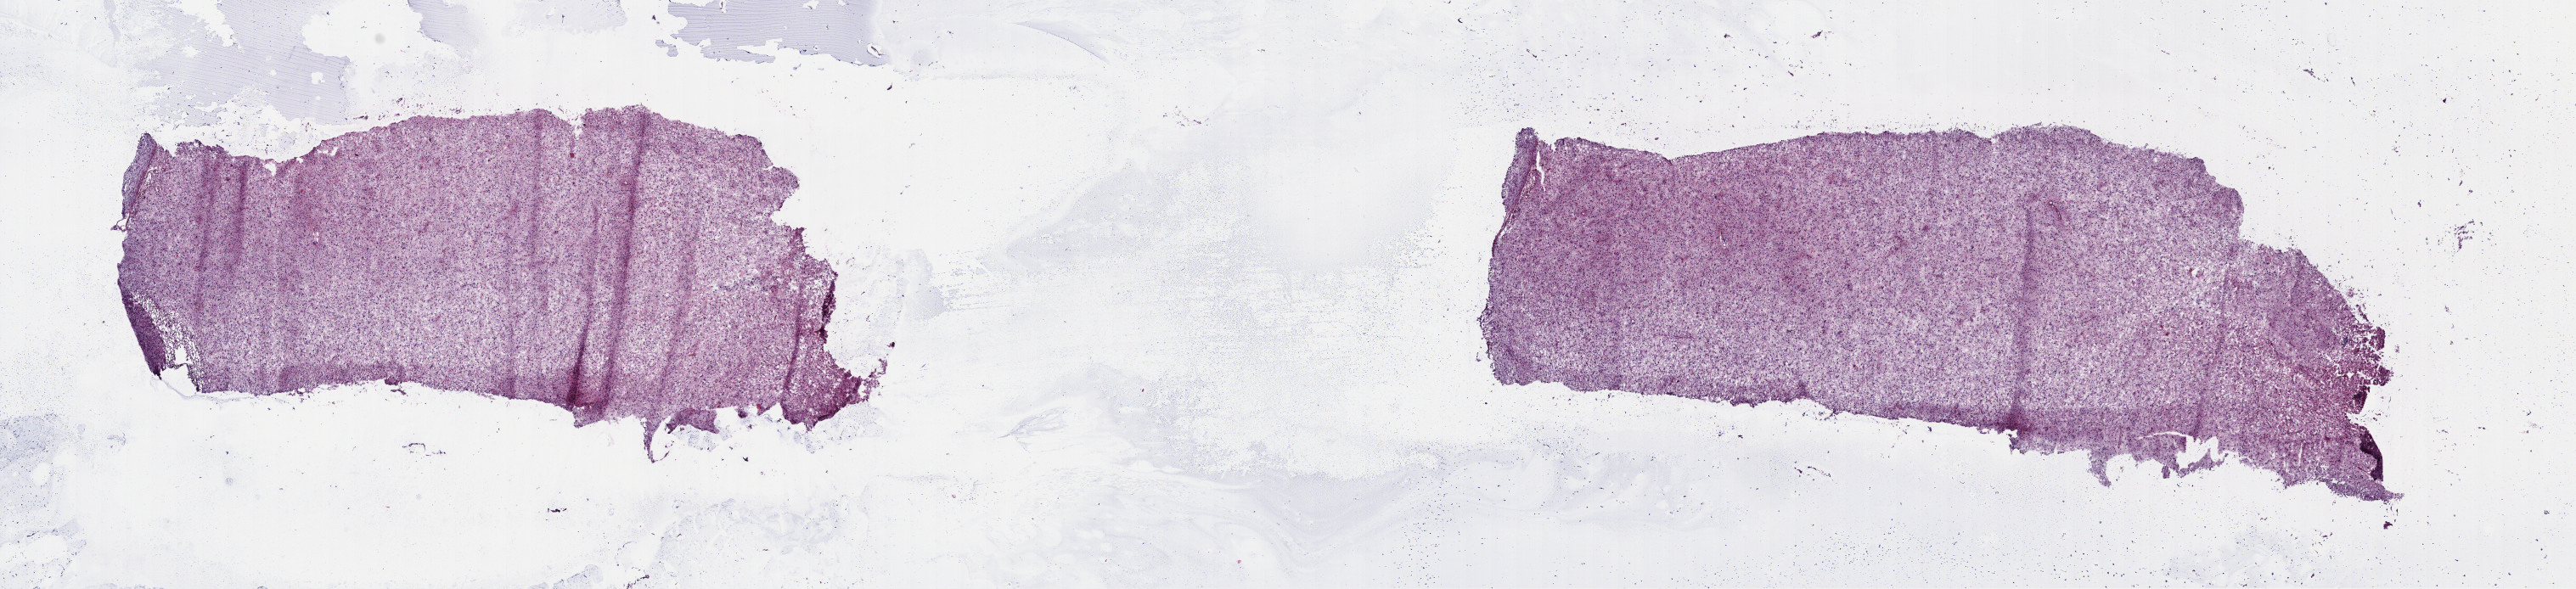
H&E whole-slide image — a low-resolution overview of the entire scanned area, about 23.8 x 5.5 mm, frozen section from the top of the tissue portion, primary tumour sample from the brain. Patient: male, age at initial diagnosis 26 years. Histologic grade: G2 (moderately differentiated). Pathologist review of this section (percent, as recorded): tumour cells 80%, tumour nuclei 90%, normal cells 15%, stromal cells 5%, necrosis 0%. Infiltration values recorded for this section: lymphocyte infiltration 0%, monocyte infiltration 0%, neutrophil infiltration 0%.
* laterality: left
* histologic diagnosis: Mixed glioma